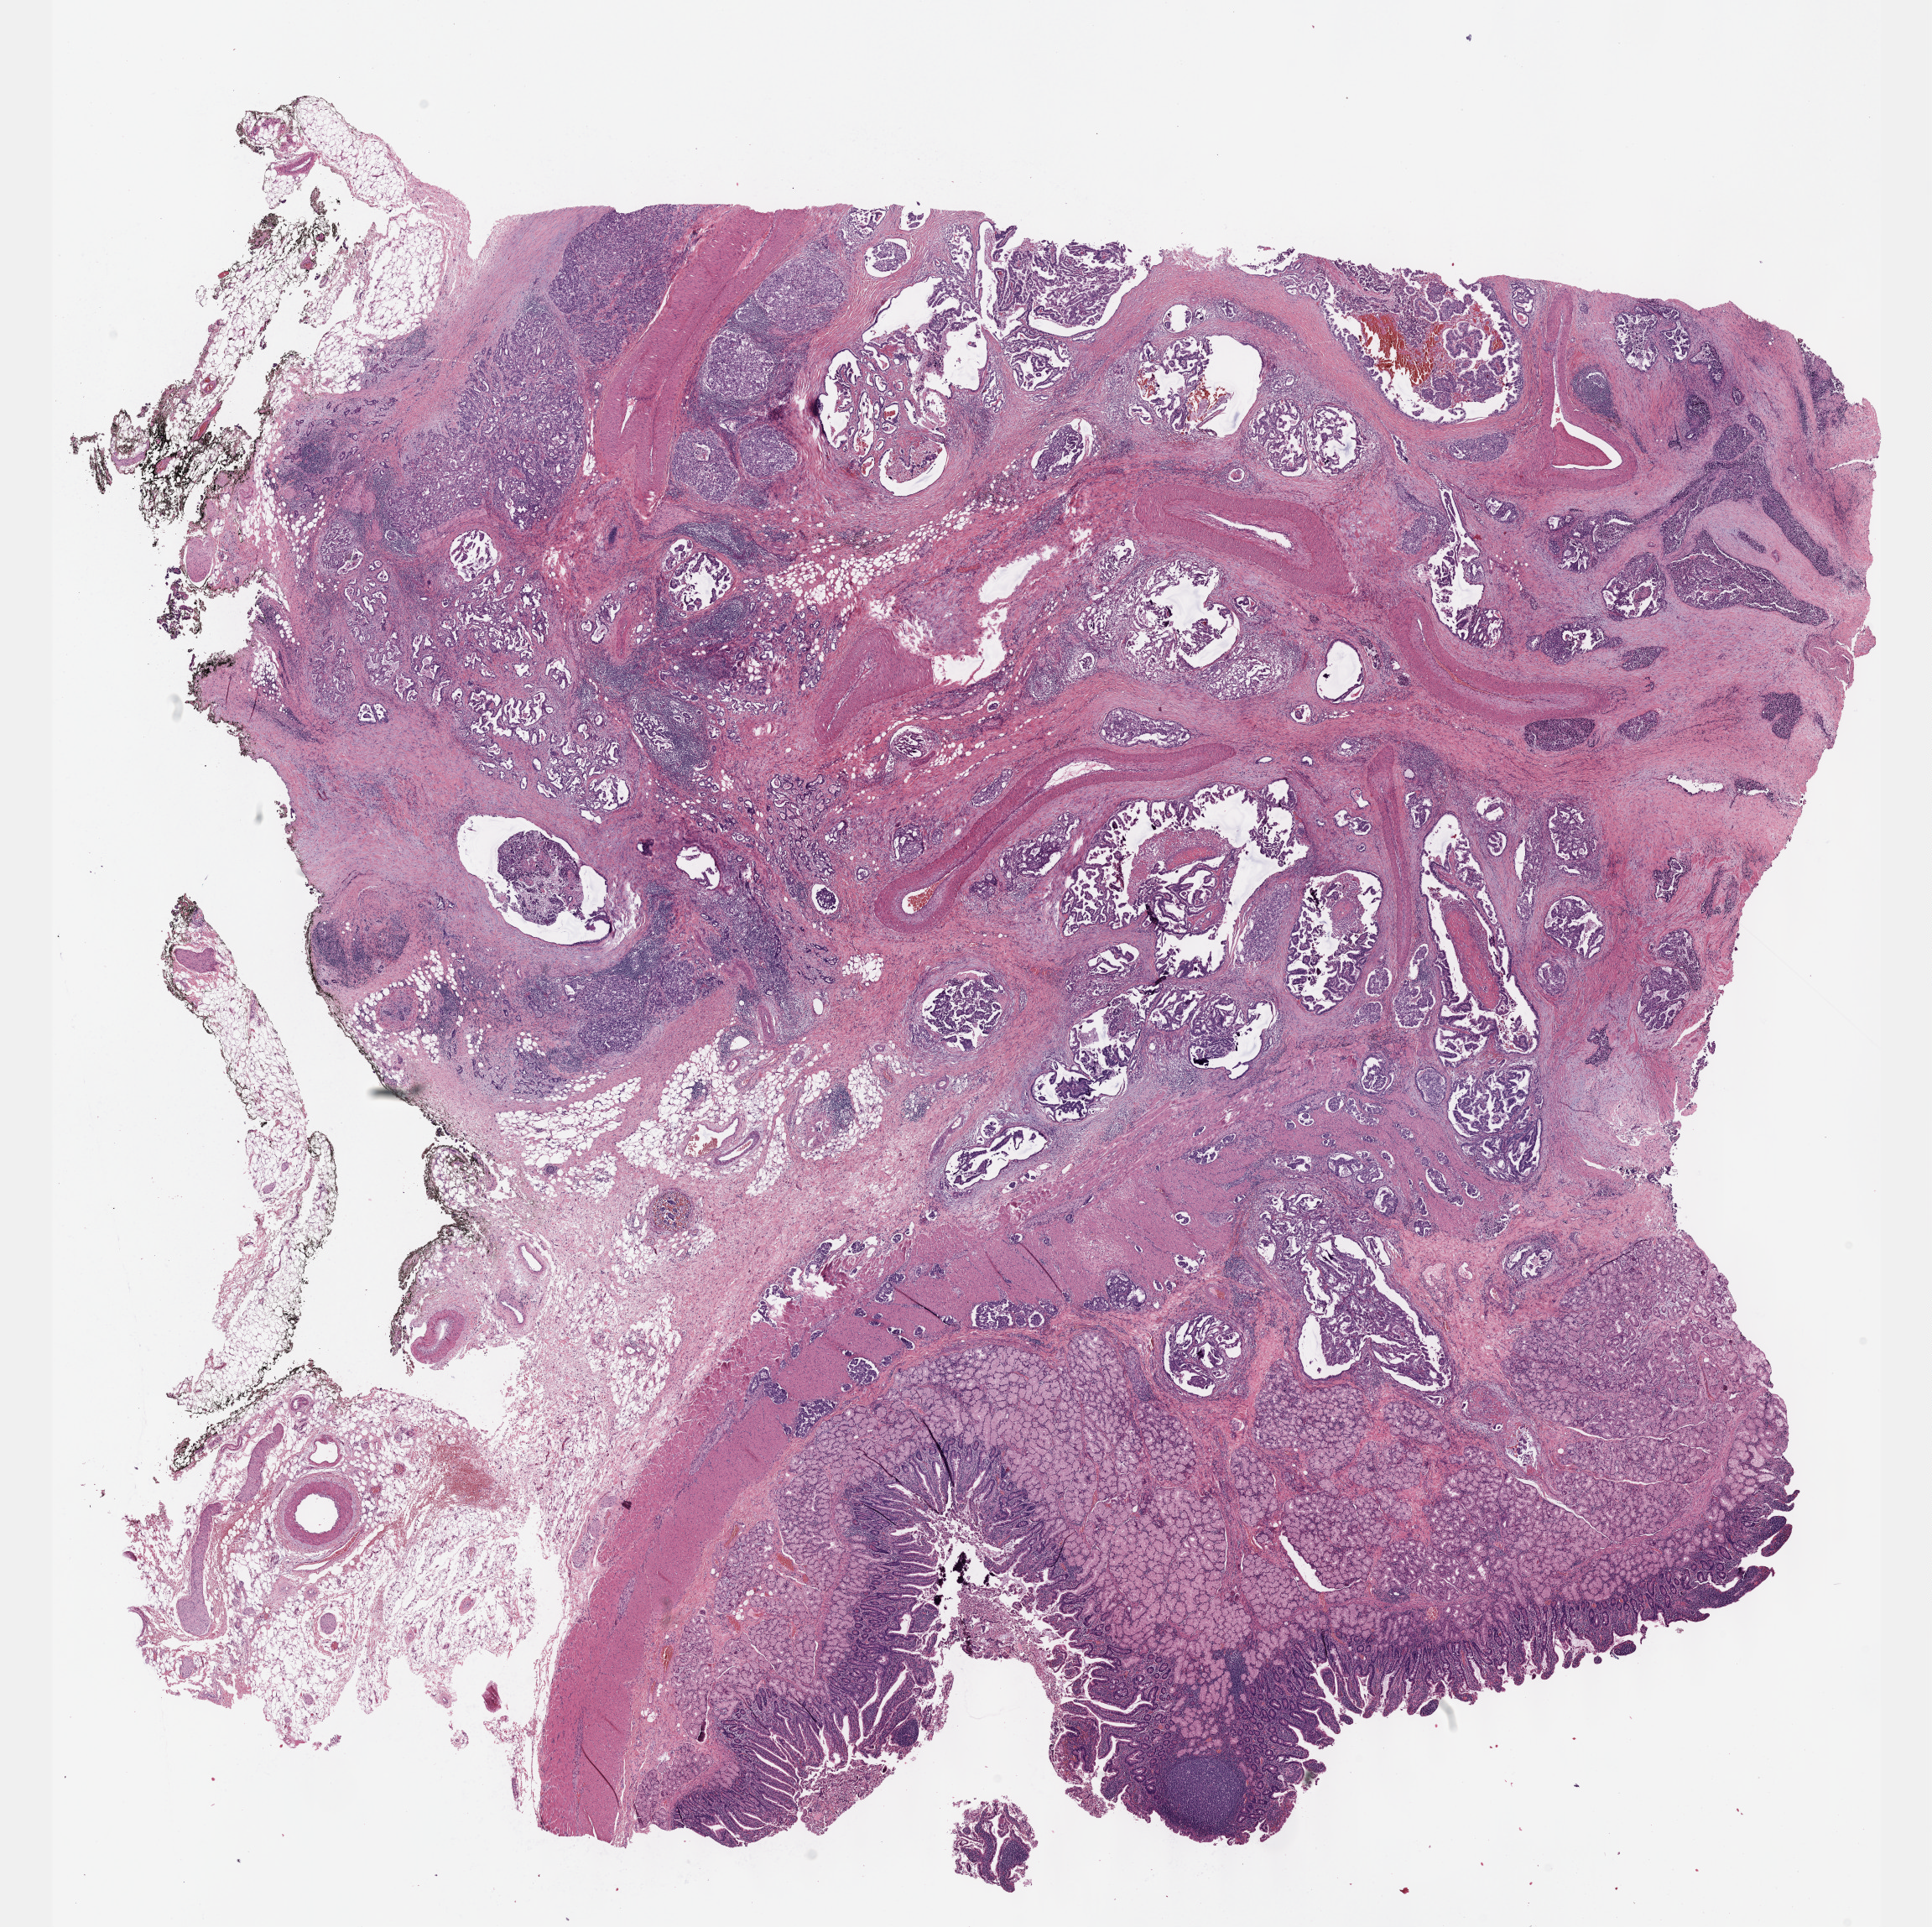
H&E whole-slide image — low-resolution overview of the scanned area, about 18.6 x 18.6 mm, FFPE section, sample: primary tumour, stomach. Male, age 49 years at initial diagnosis. Histologic grade: G2 (moderately differentiated).
- AJCC pathologic stage: IV
- pathologic diagnosis: Papillary adenocarcinoma, NOS
- lymph nodes positive (case pathology): 32 of 81 examined
- TNM: T3 N3 M0